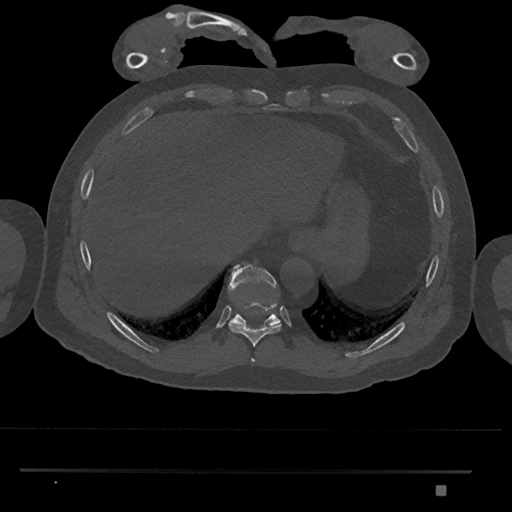
CT including the spine, one axial slice; slice 1036 of 1134 in the series (ordered by position); reconstruction kernel Br40s/3; 120 kVp; bone window (W 1800 / L 400 HU); 0.5 mm slice thickness; 512 × 512 image matrix. Male patient, age 65 years. From the clinical record (not read from this slice): primary cancer: prostate.
Annotated regions visible in this slice (semi-automatic segmentation, software-assisted and operator-edited):
- T10 vertebra: bounding box (x1, y1, x2, y2) in pixels: (228, 264, 281, 328)
- T8 vertebra: (252, 358, 255, 362)
- T9 vertebra: (228, 300, 281, 347)